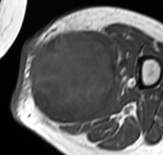
MRI of an extremity soft-tissue mass, one axial slice. Slice 33 of 65 in the series (ordered by position). MR volume resampled by the dataset authors to the PET/CT grid (not the native acquisition matrix). 3.27 mm slice thickness. 163 × 155 image matrix, field of view 159 × 151 mm. Female patient. Case-level facts recorded for this patient, not image findings: histological type: pleomorphic leiomyosarcoma; grade: high; site of the primary tumour: left thigh.
Outlined on this slice (expert contour drawn on MRI and transferred to this co-registered scan by the dataset authors):
- gross tumour volume including surrounding oedema: bounding box (x1, y1, x2, y2) in pixels: (26, 29, 120, 128)
- gross tumour volume (mass): (26, 31, 116, 125)